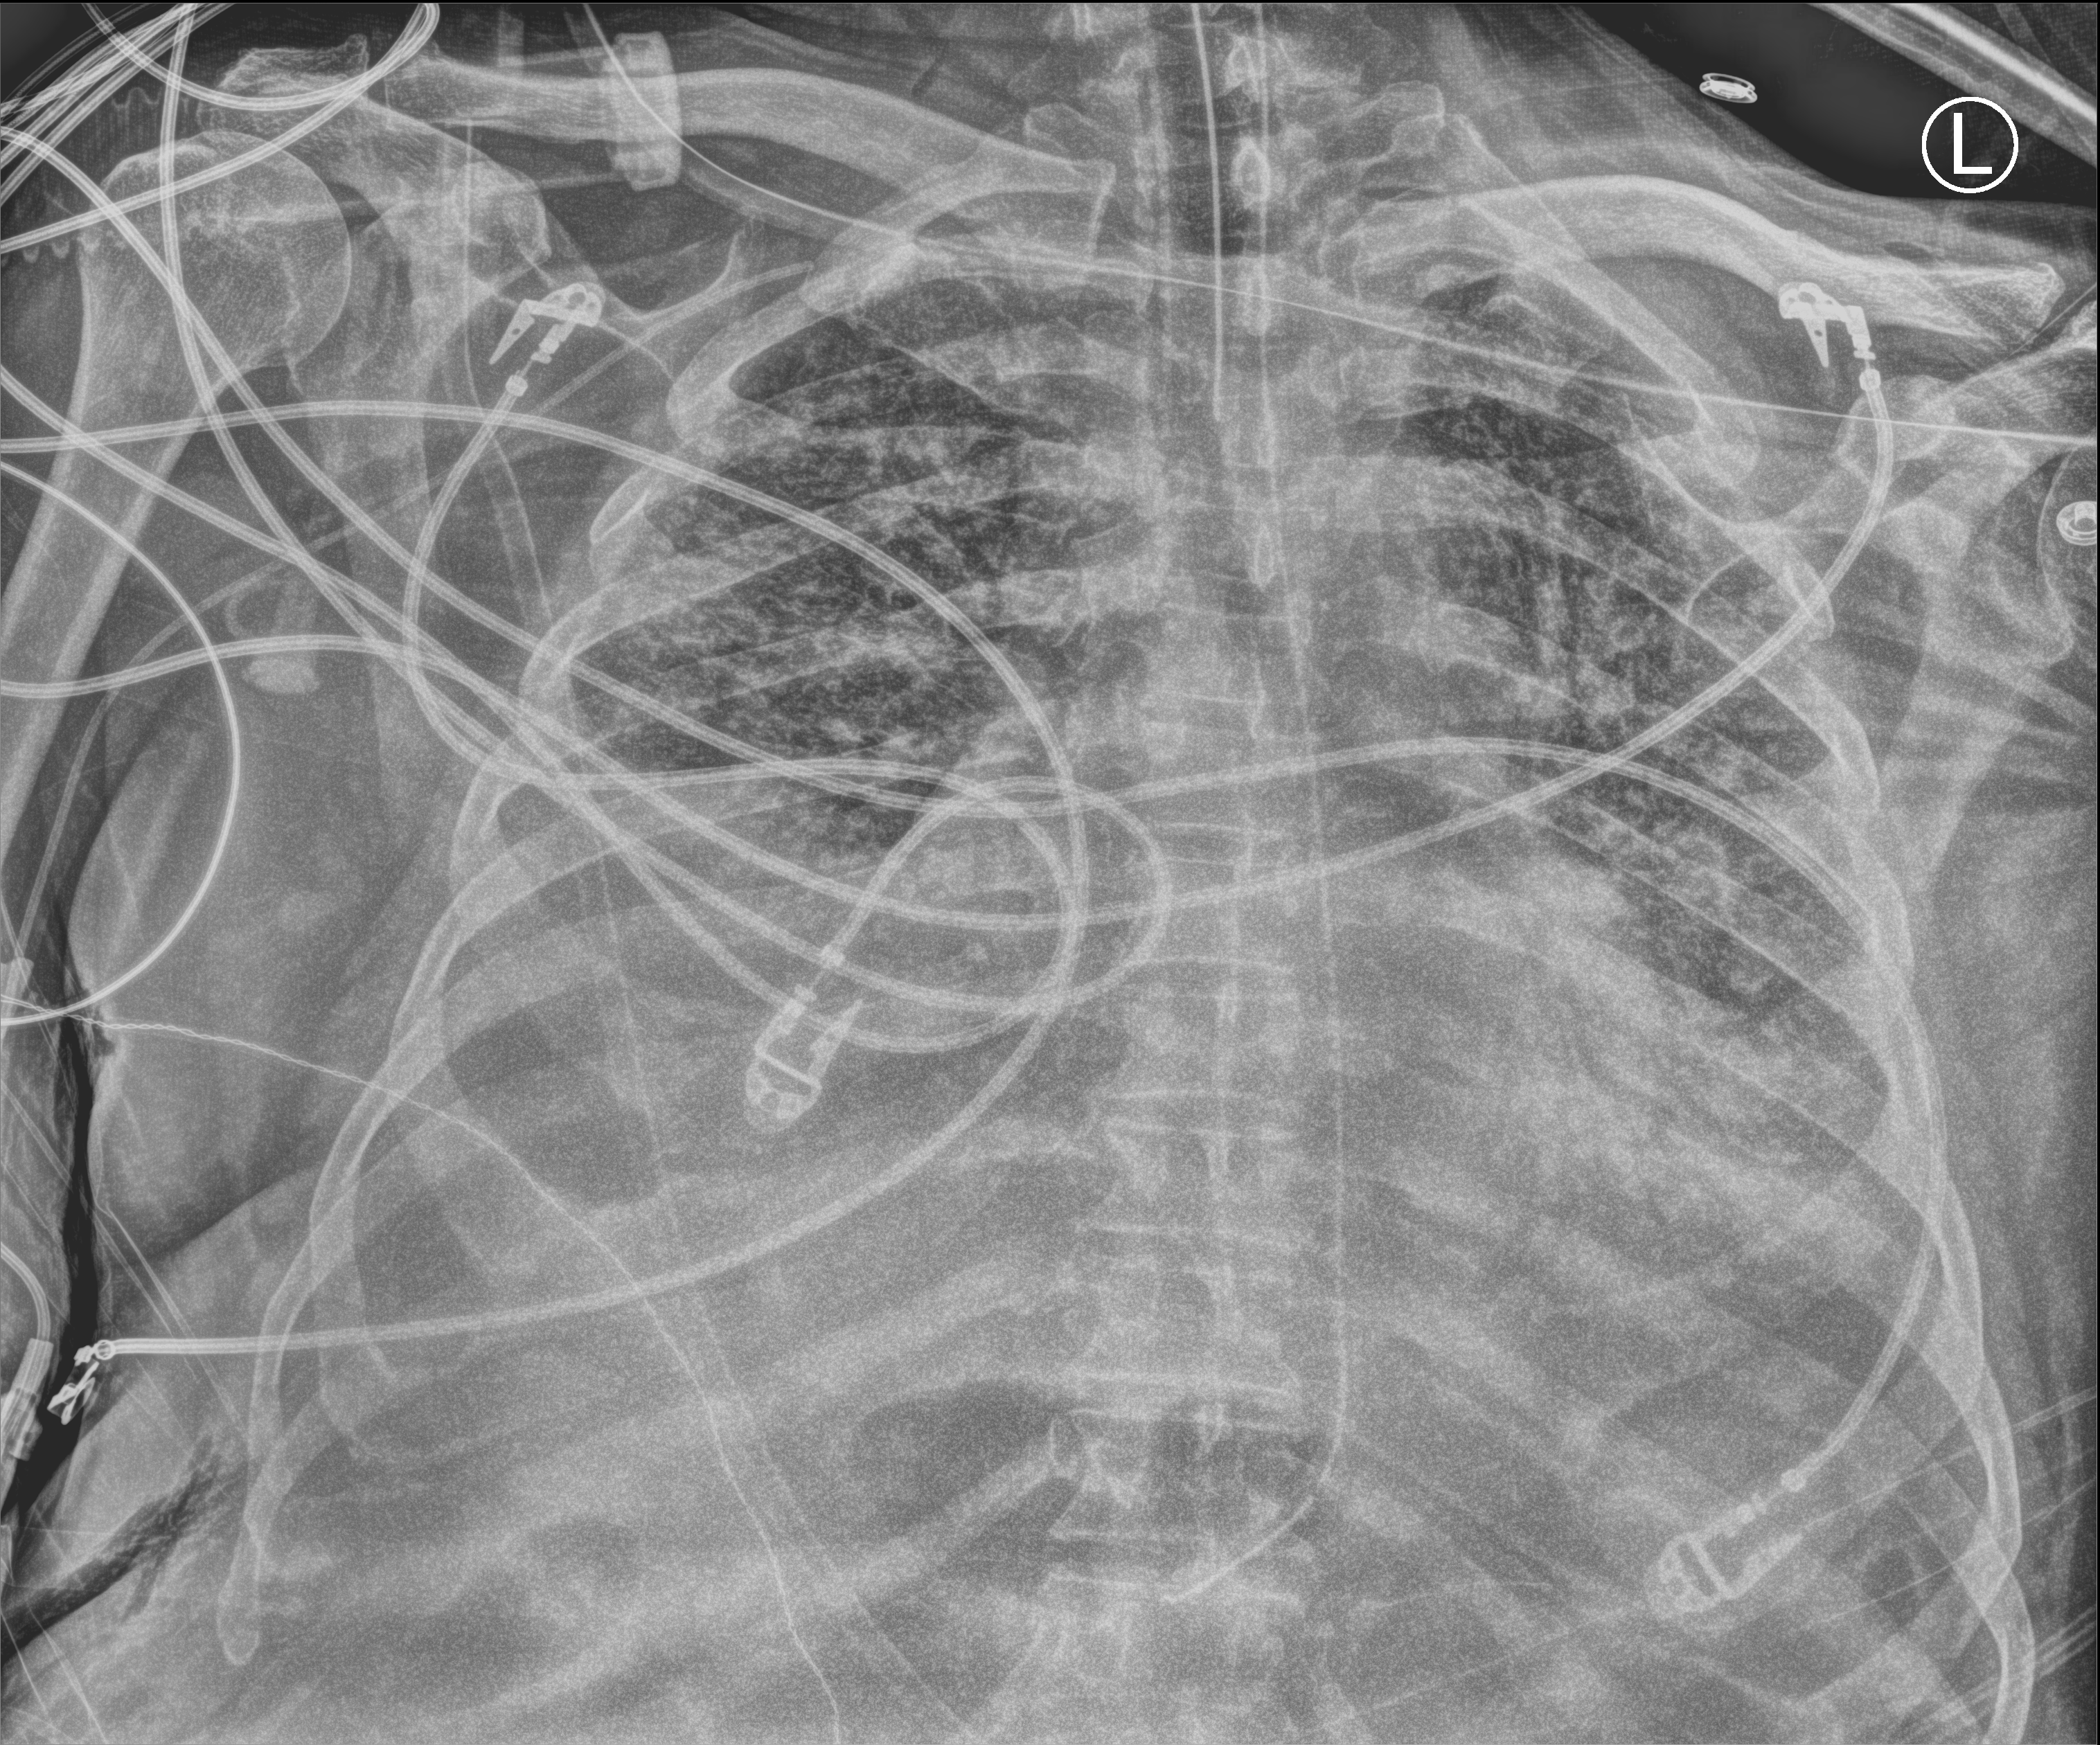
Chest X-ray (portable); anteroposterior (AP) projection. Male patient hospitalised with COVID-19, age 60–74 years.
Hospital-stay facts (about this admission, not read from this image; timing relative to this image not recorded):
- COPD (admission record): no